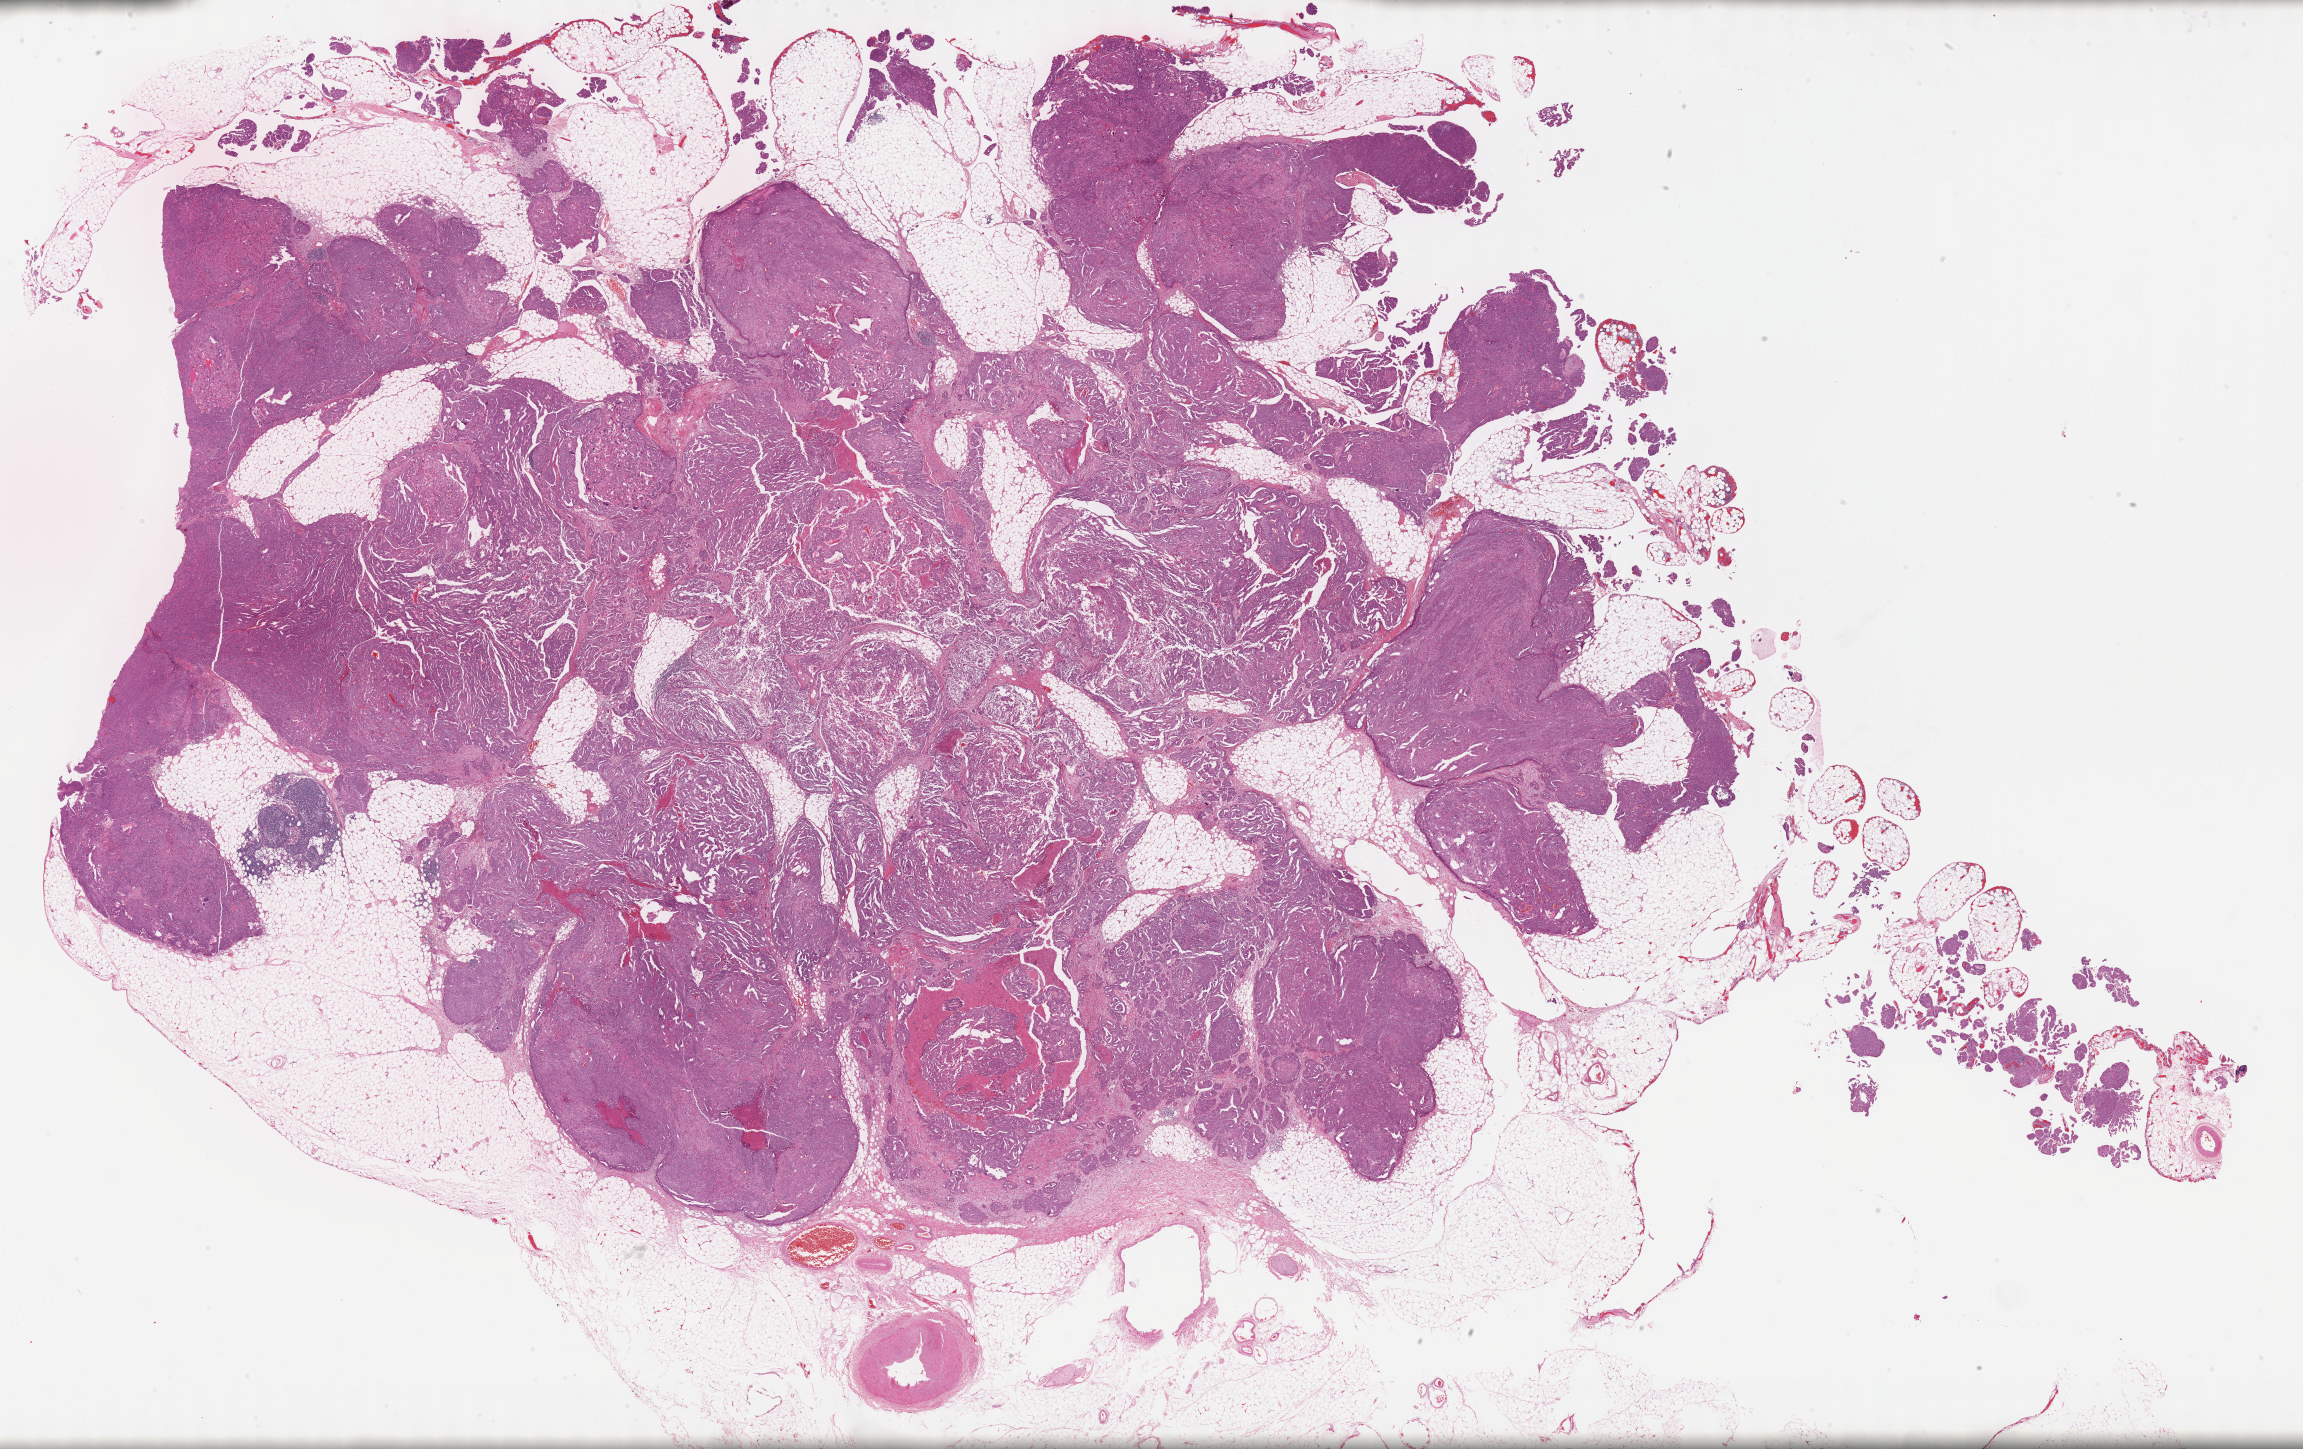
Digitized H&E tissue section (whole slide), whole scanned area (about 37.2 x 23.4 mm, slide scanned at 40x) shown as a low-resolution overview, FFPE section, sample: primary tumour, ovary. Female, age 85 years at initial diagnosis. Histologic grade: G3 (poorly differentiated).
FIGO stage: IIIC. Diagnosis: Serous cystadenocarcinoma, NOS.